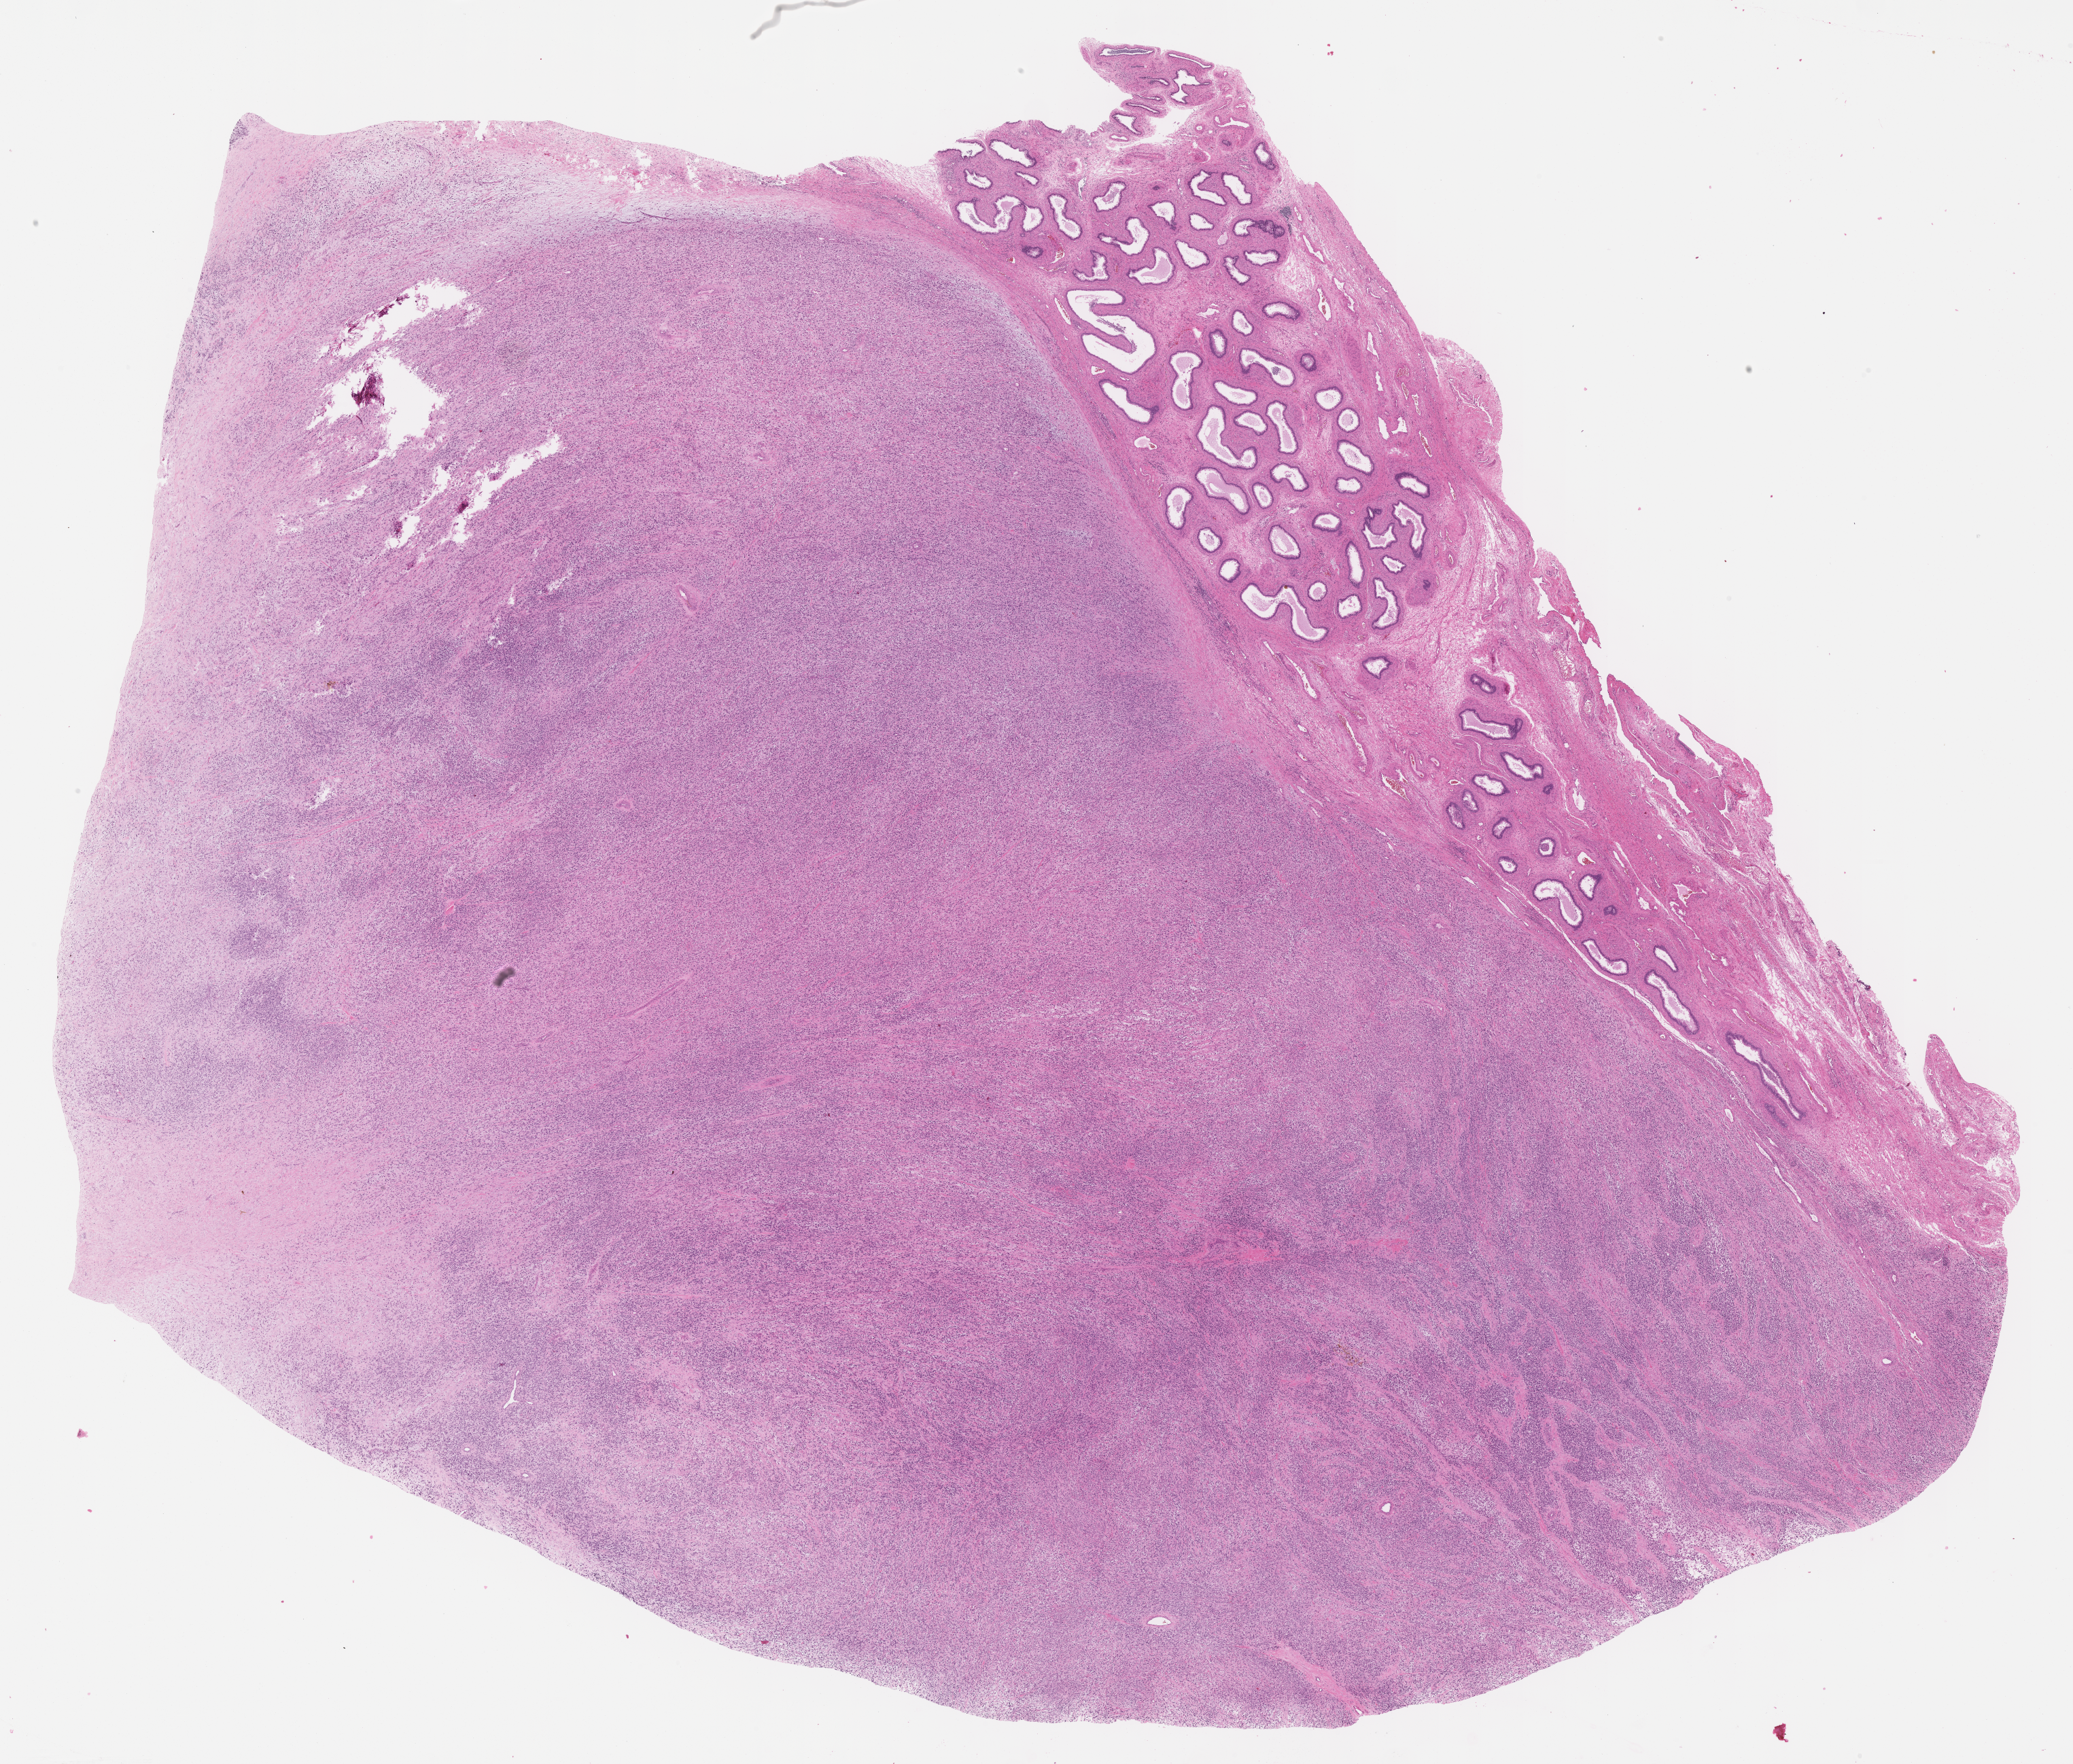
Hematoxylin and eosin (H&E) whole-slide image of tumor tissue — shown as a low-resolution overview of the whole scanned area (about 24.7 x 21.0 mm), FFPE section, sample anatomic site: paratesticular, right. Patient: male, age 16.2 years at diagnosis.
Diagnosis: rhabdomyosarcoma; histological classification: embryonal rhabdomyosarcoma. Primary site (case record): testis-paratesticular. Stage (as recorded): 1.